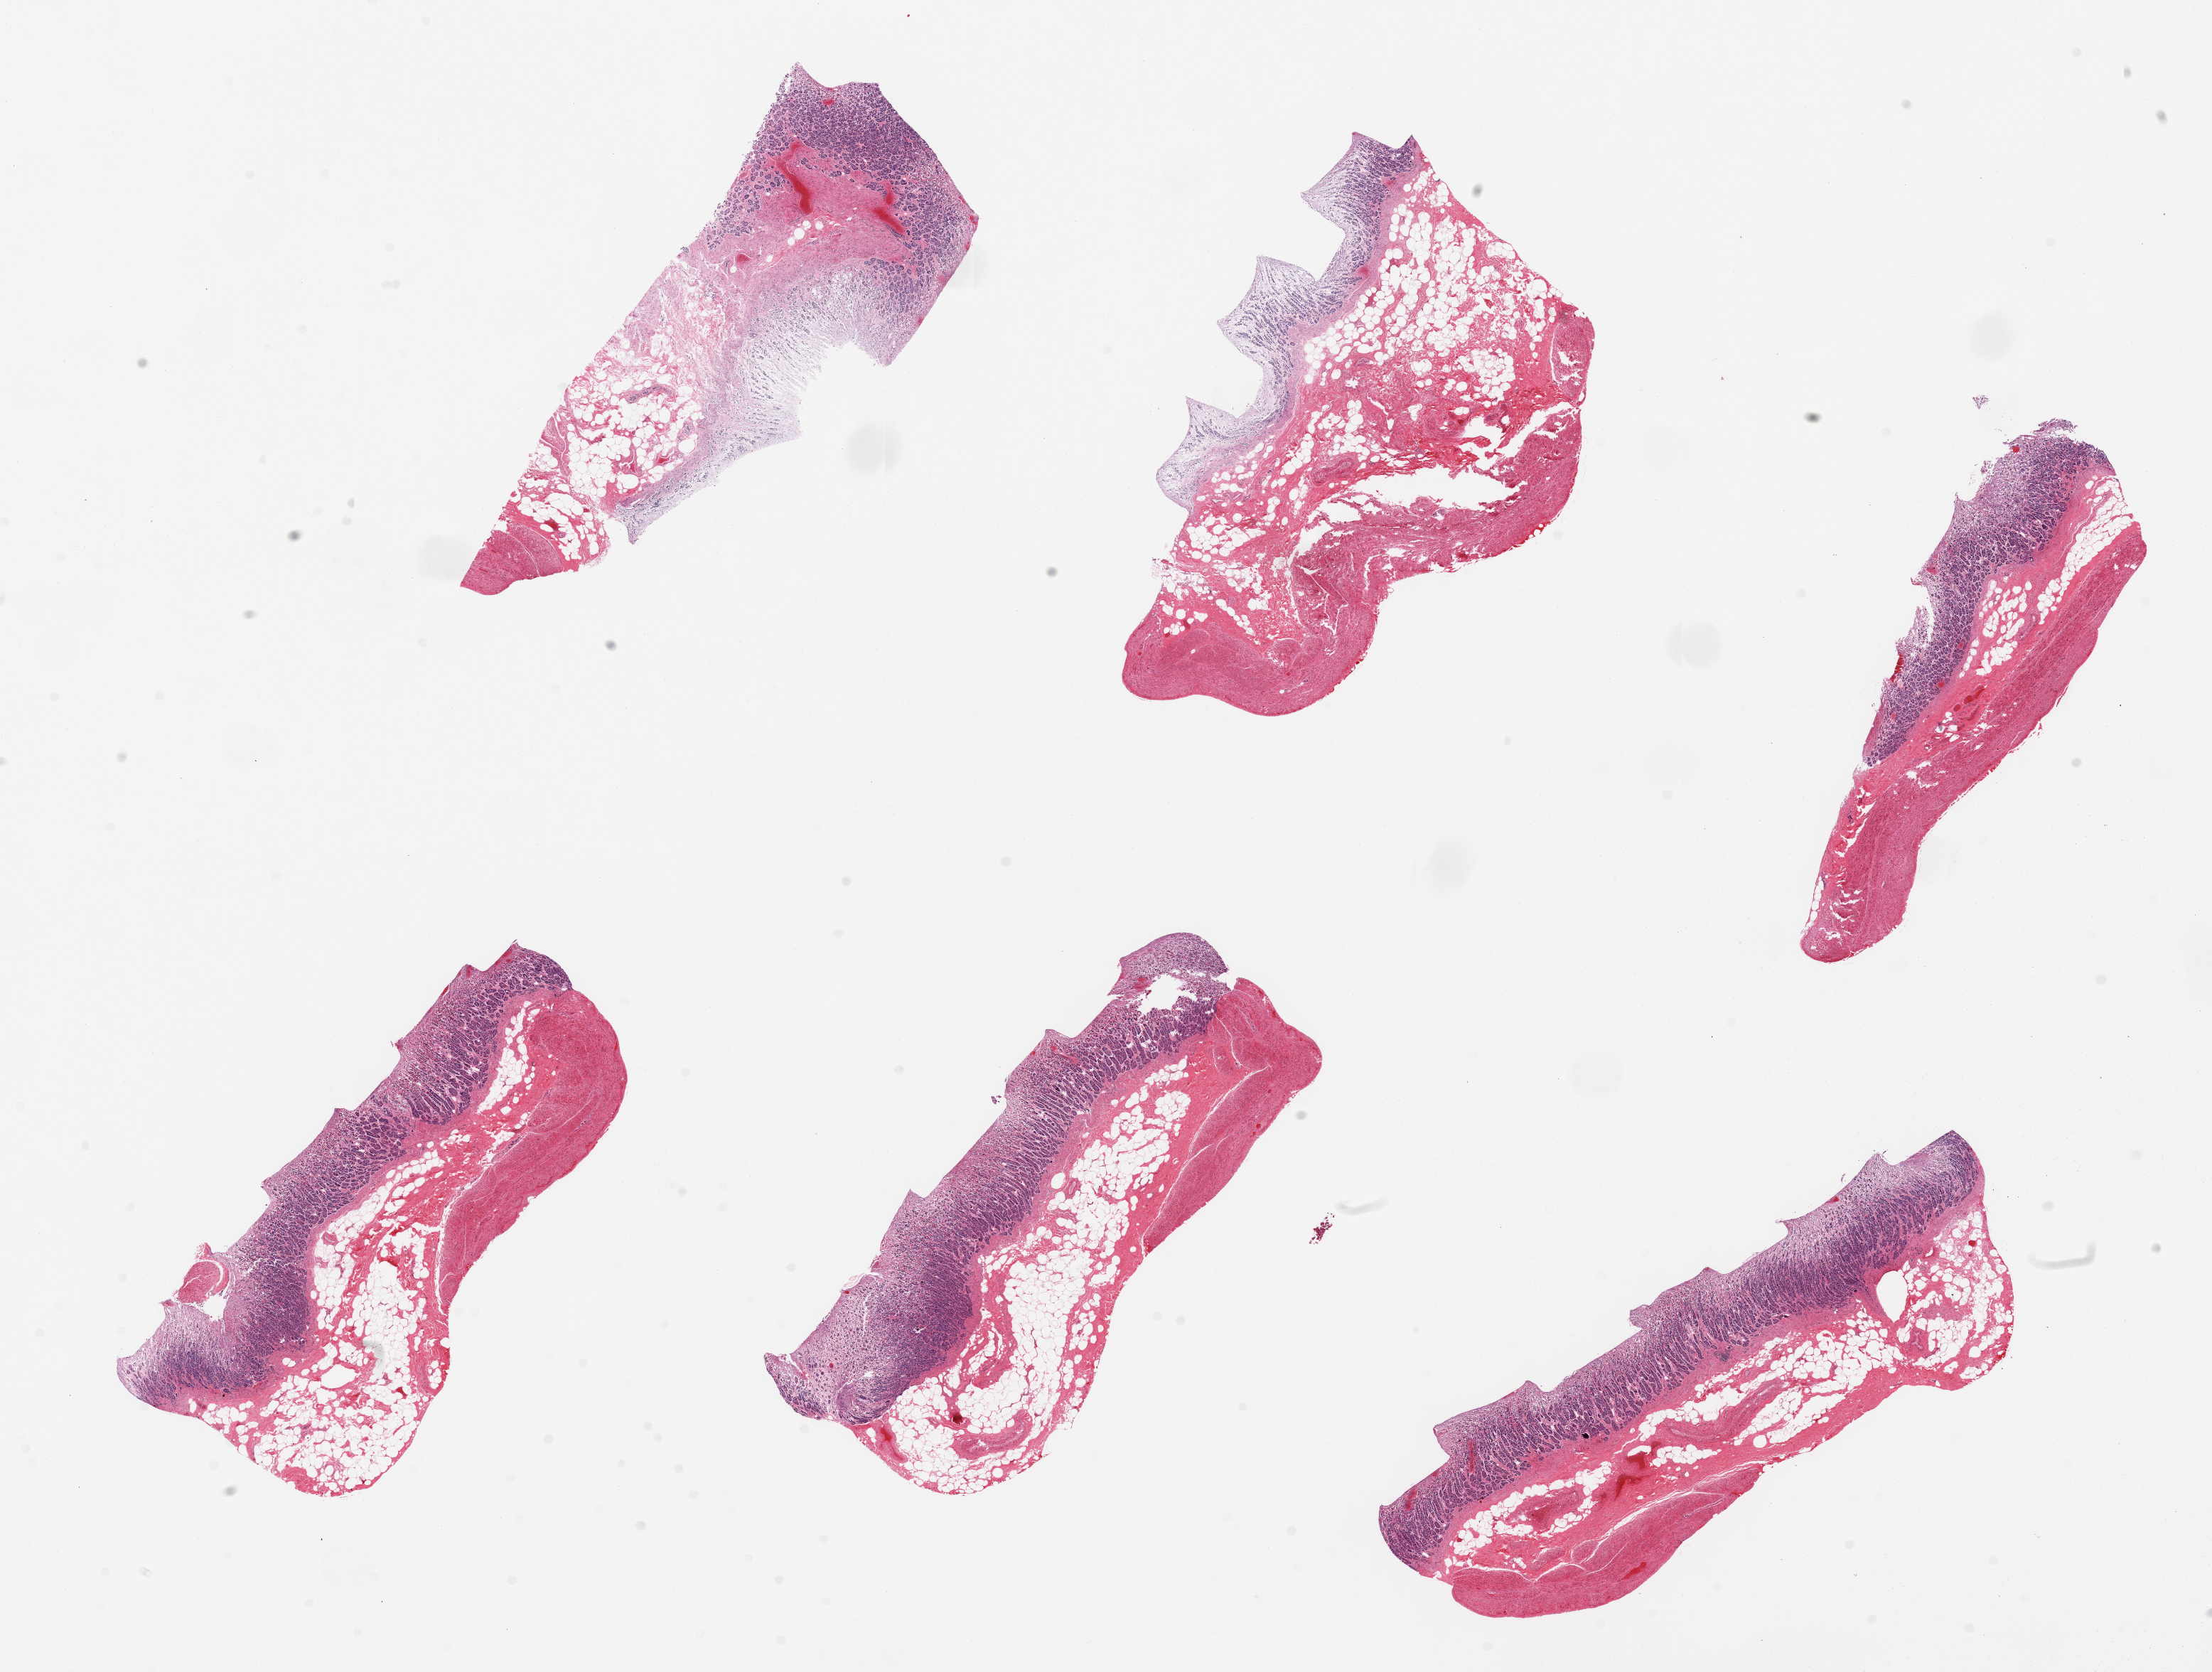
Whole-slide image, hematoxylin and eosin (H&E) stain — a low-resolution overview of the entire scanned area, about 24.6 x 18.6 mm. PAXgene-fixed paraffin-embedded (PFPE) section. Target tissue: stomach. Tissue donor sample. Male donor.
Reviewer comment on this tissue sample: 6 pieces, mucosa (moderately to severely autolyzed) and muscularis.